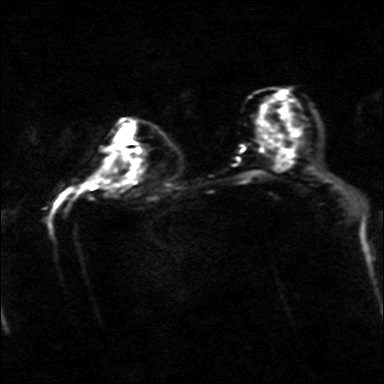
Breast MRI, one axial slice; position 21 of 40 along the scan axis; diffusion-weighted series; image 2 of 4 stored at this slice position (different b-values; order by instance number); 3 T; 384 × 384 image matrix, field of view 320 × 320 mm. Female patient.
Outlined on this slice (outlined manually by an expert reader):
- tumour on diffusion-weighted imaging: bounding box [x1, y1, x2, y2] px = [122, 141, 134, 153]